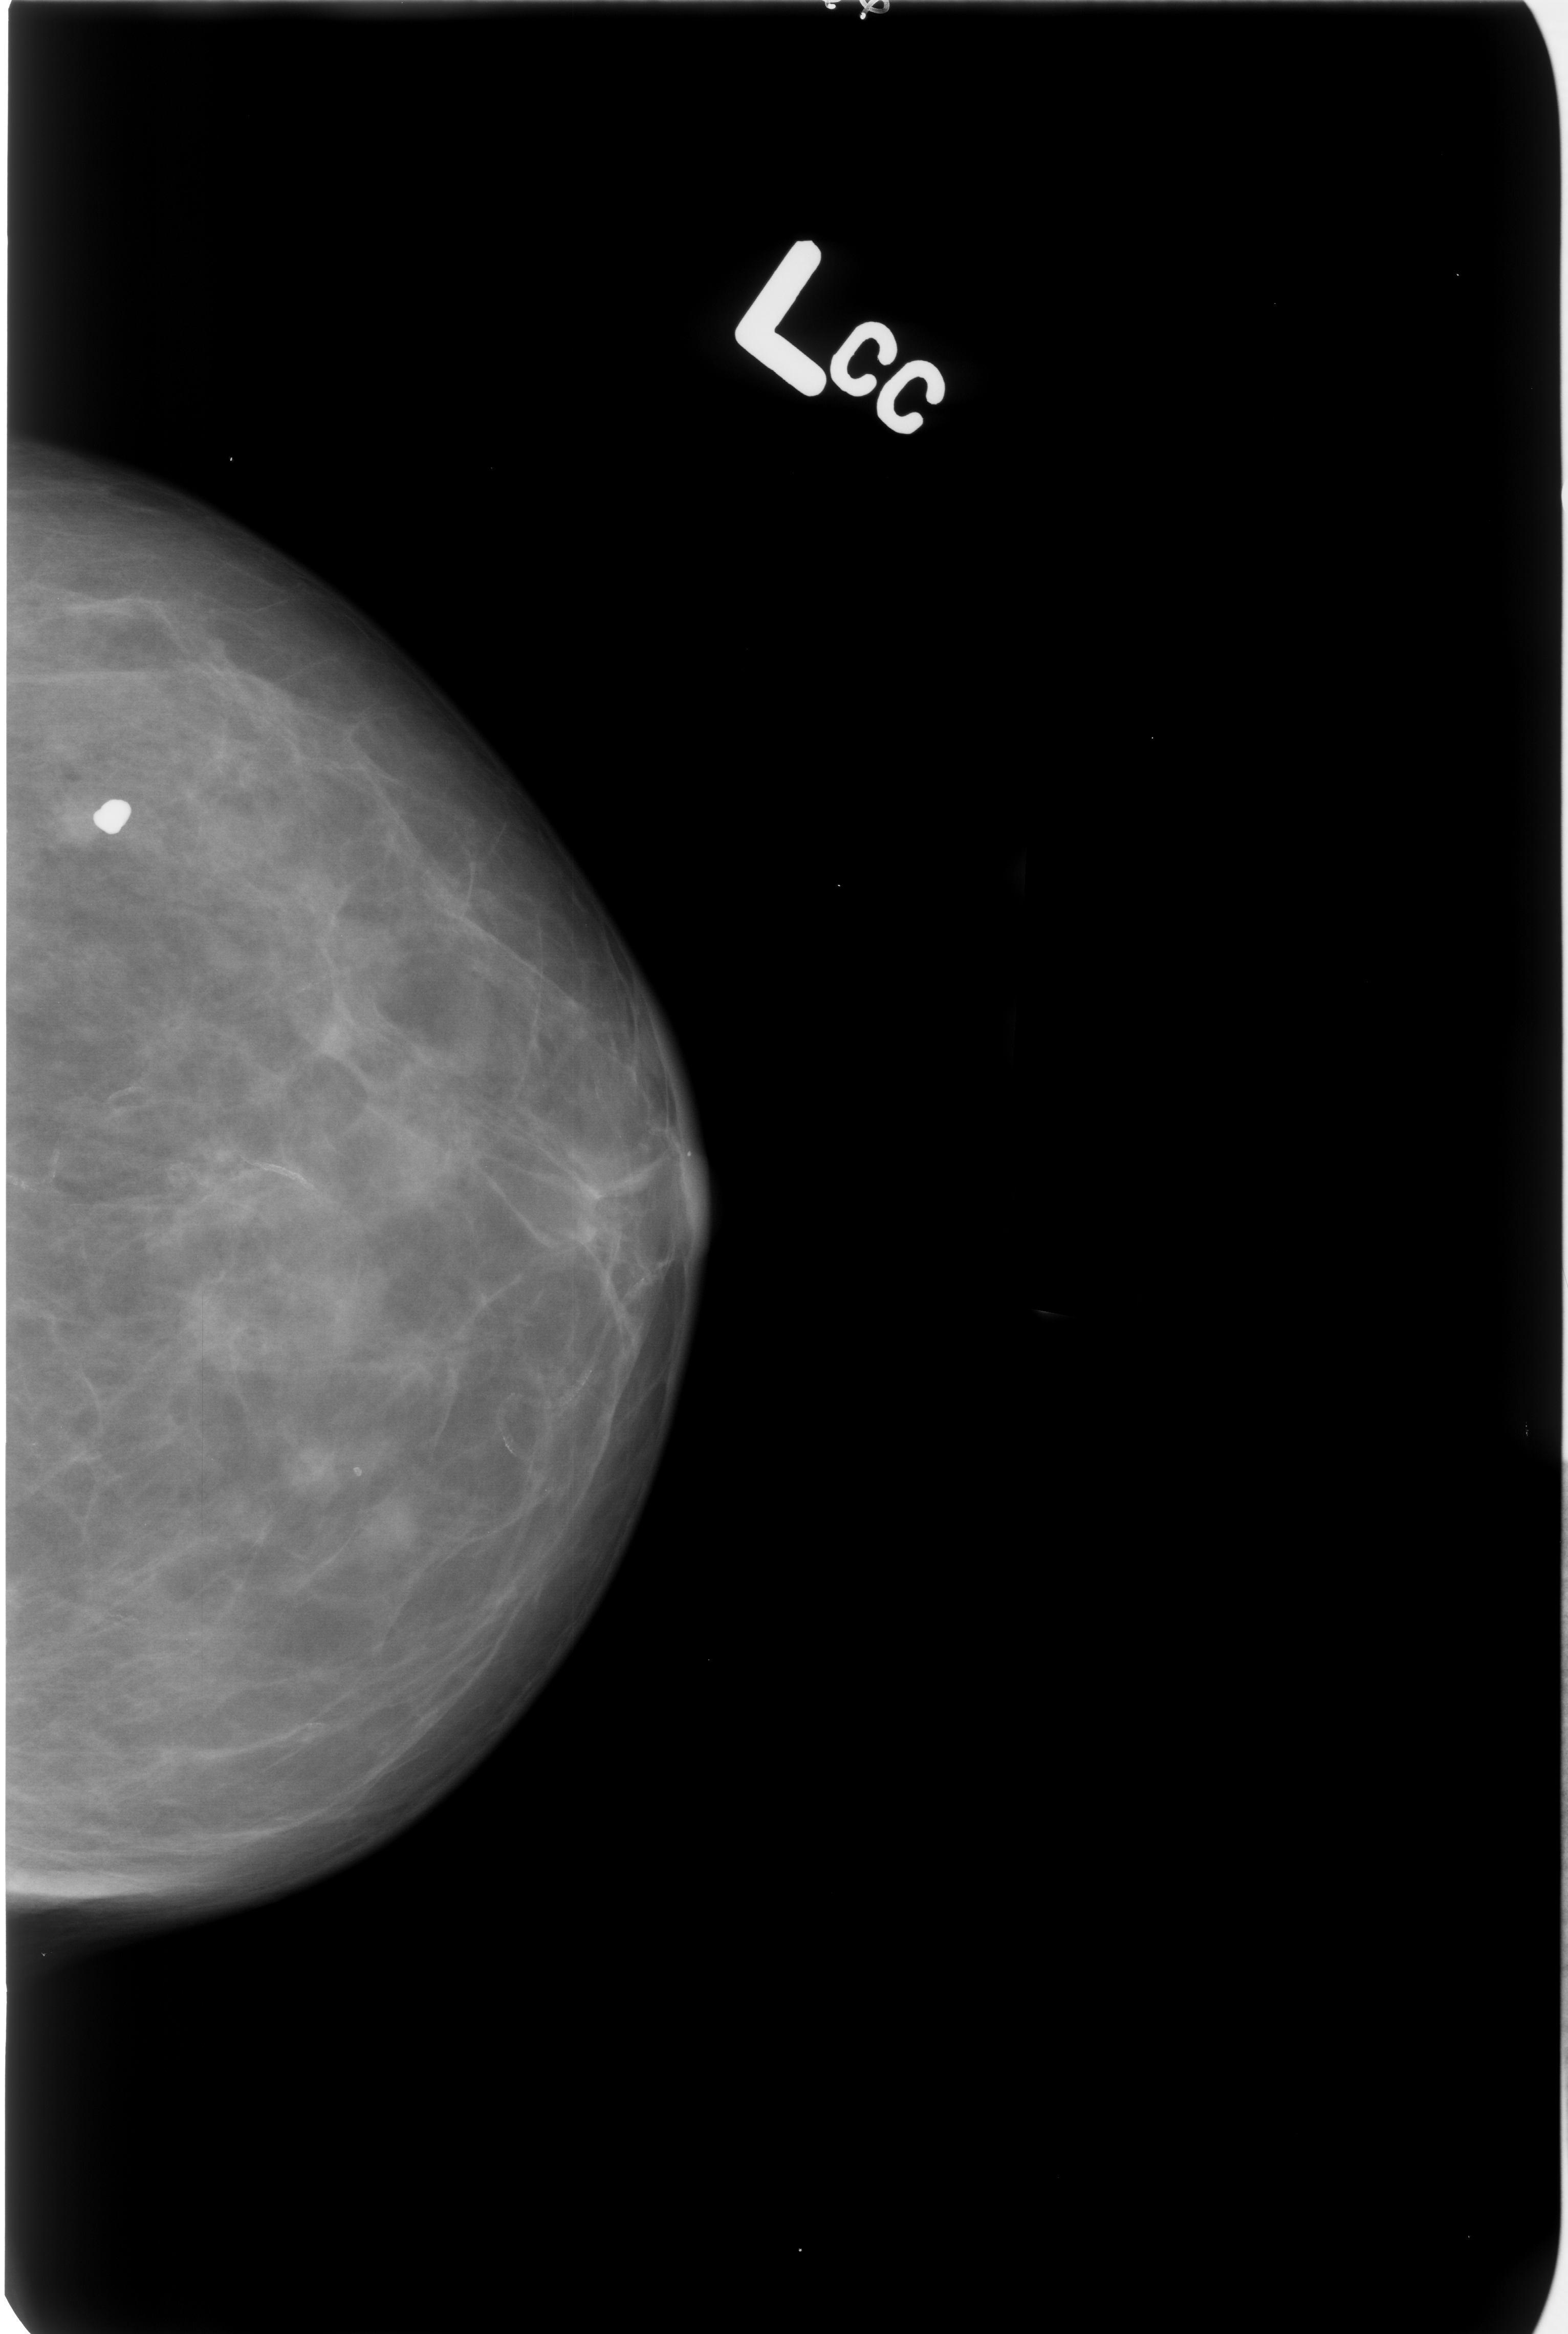
Mammogram (digitized film), left breast, CC view, BI-RADS breast density category 2 (scale 1–4).
- Abnormality record for this image: Finding 1 of 2: calcifications, morphology coarse; BI-RADS assessment category 2; subtlety rating 5 on a 1 (subtle) to 5 (obvious) scale; benign; no additional work-up was recommended (benign without callback).
- Finding 2 of 2: calcifications, morphology vascular; BI-RADS assessment category 2; benign without callback (not worked up further).